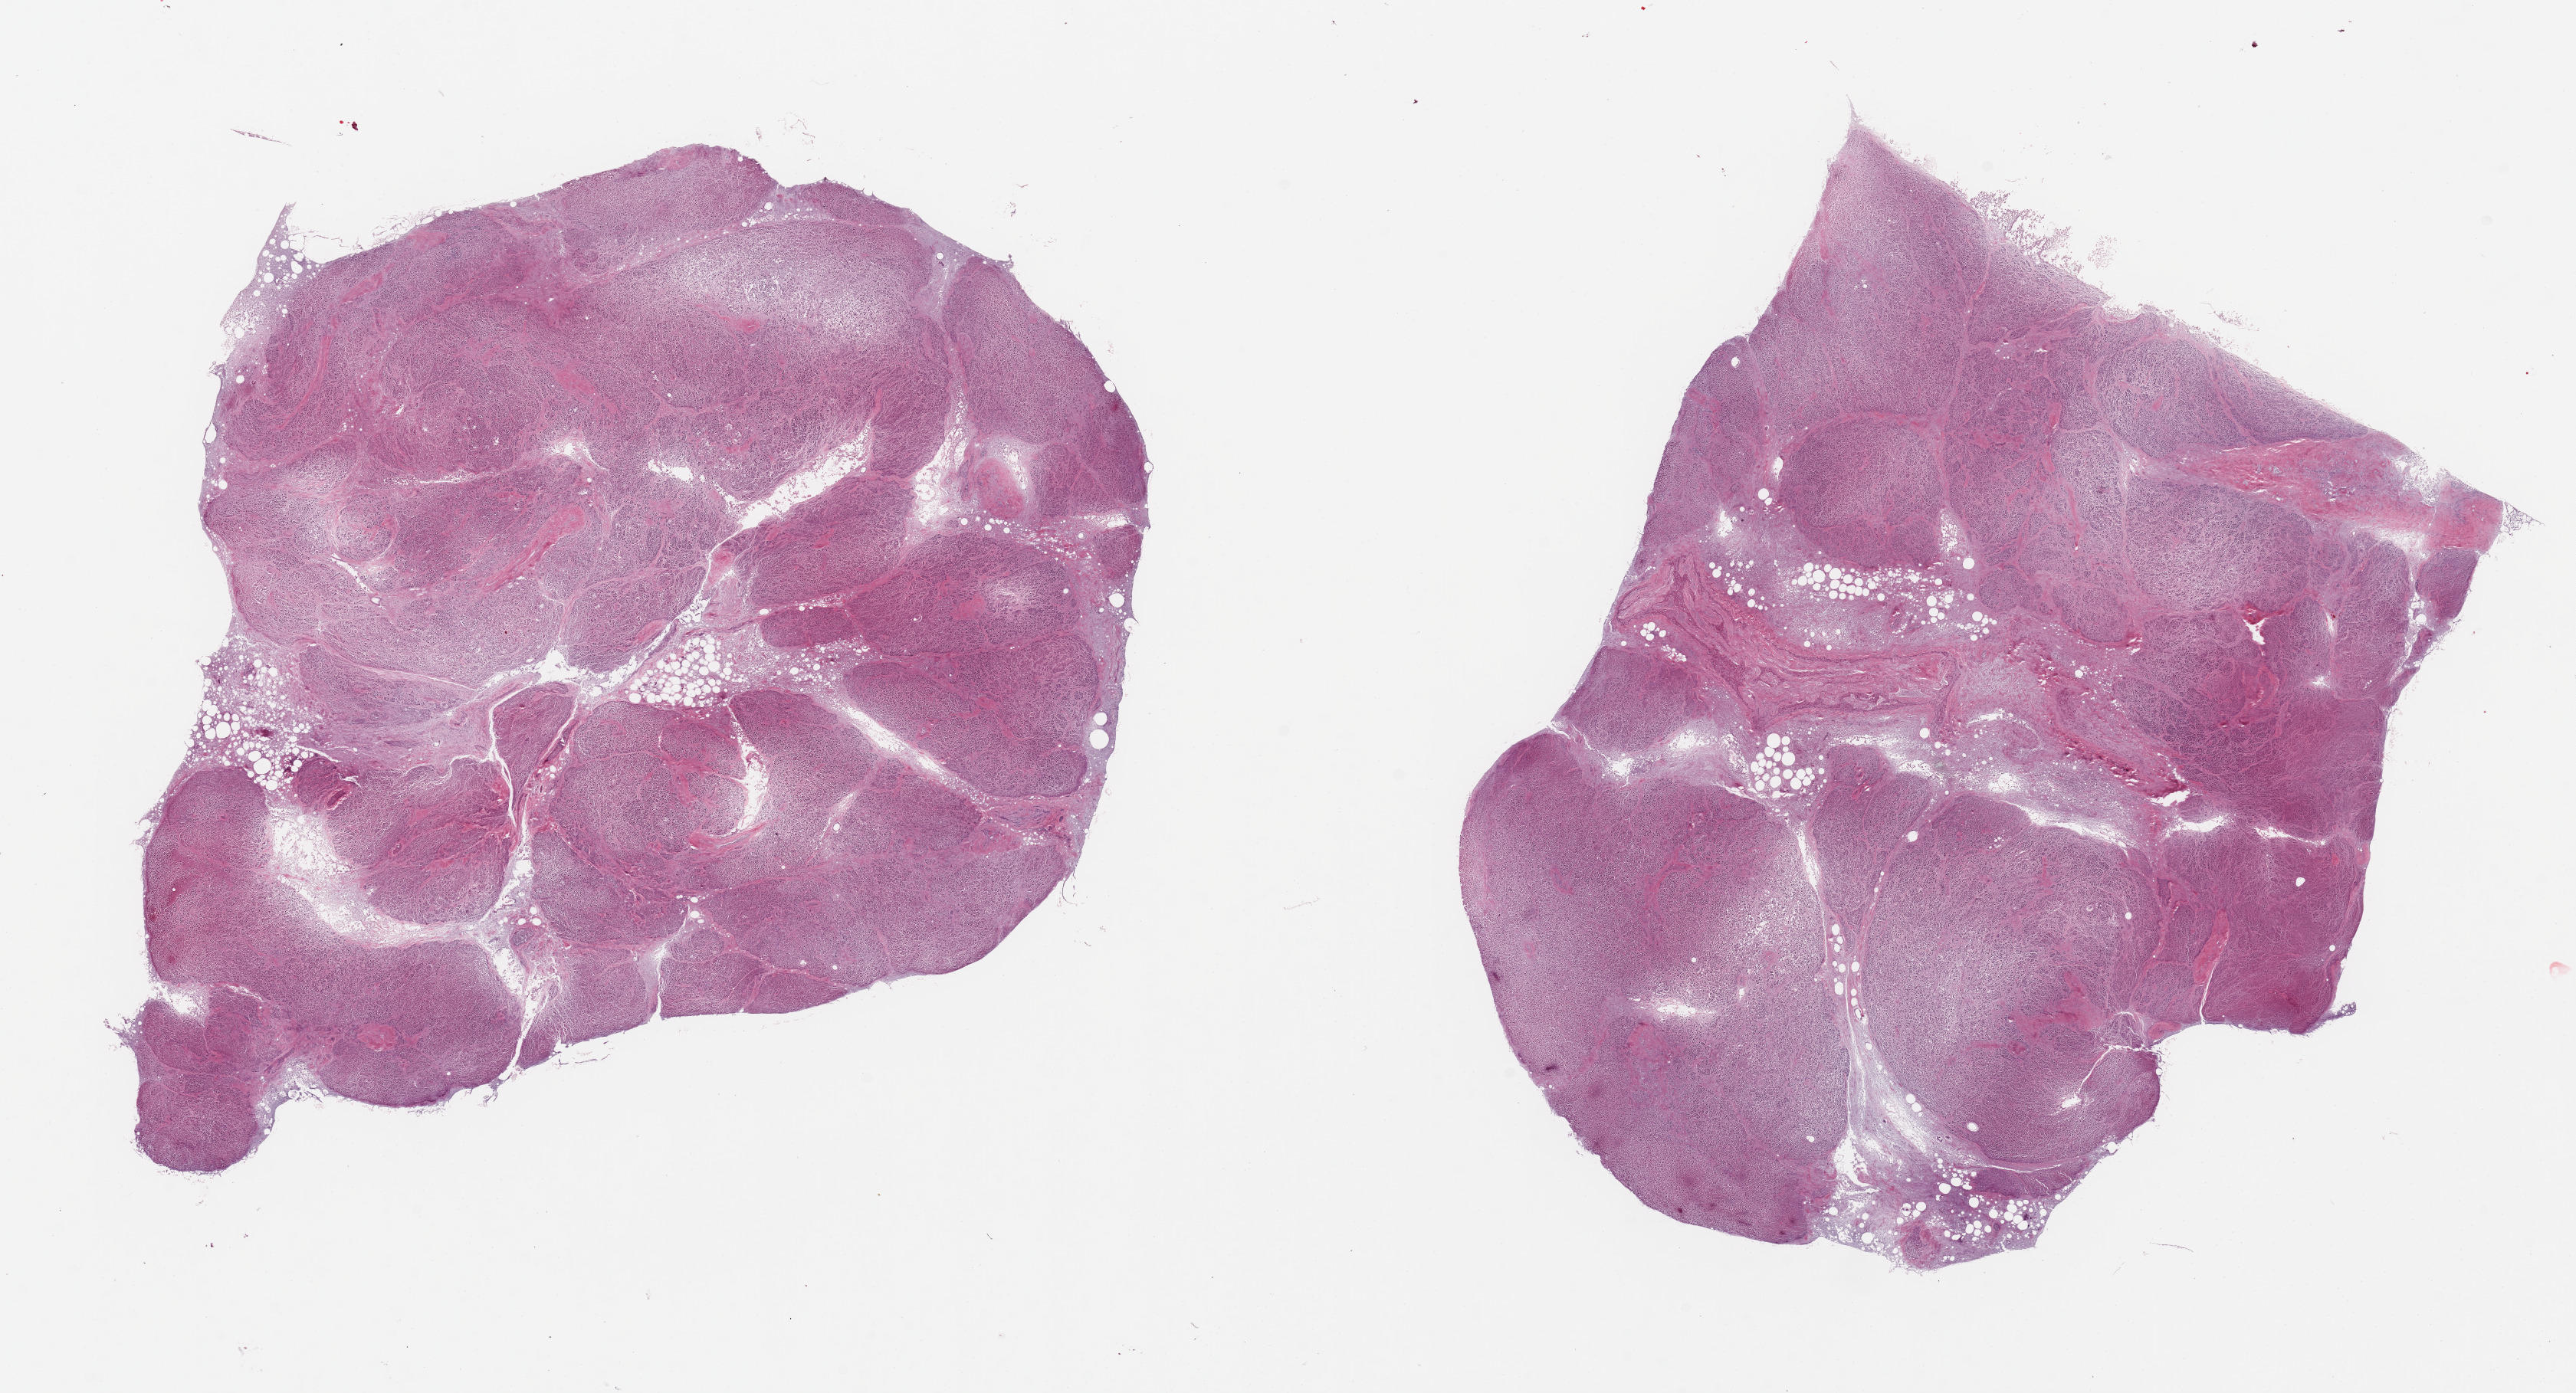
Hematoxylin and eosin (H&E) whole-slide image, shown as a low-resolution overview of the whole scanned area (about 26.6 x 14.4 mm); PAXgene-fixed paraffin-embedded (PFPE) section; target tissue: pancreas; donor tissue sample. Donor sex: male.
Reviewer comment on this tissue sample: 2 pieces, severely autolyzed.